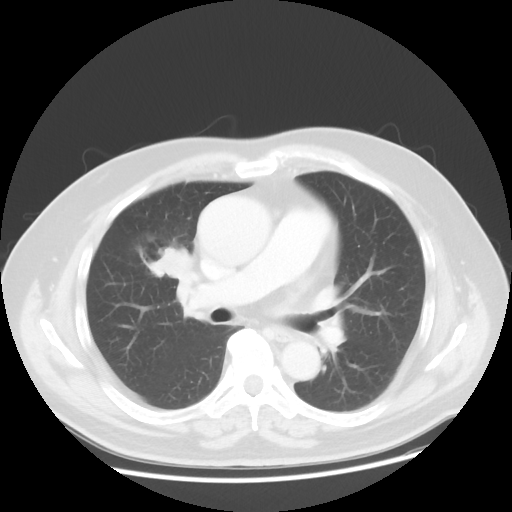
Chest CT, one axial slice; position 26 of 48 along the scan axis; reconstruction kernel STANDARD; 120 kVp; lung window (W 1500 / L -600 HU); 5 mm slice thickness; 512 × 512 image matrix. Male patient, age 60 years. From the clinical record (not read from this slice): clinical TNM (as recorded): T2 N3 M0; histopathological grade: G2-3.
Structures marked on this image (rectangle marked by the reading radiologist):
- lung tumour (recorded histology: adenocarcinoma): bounding box (x1, y1, x2, y2) in pixels: (135, 234, 192, 288)